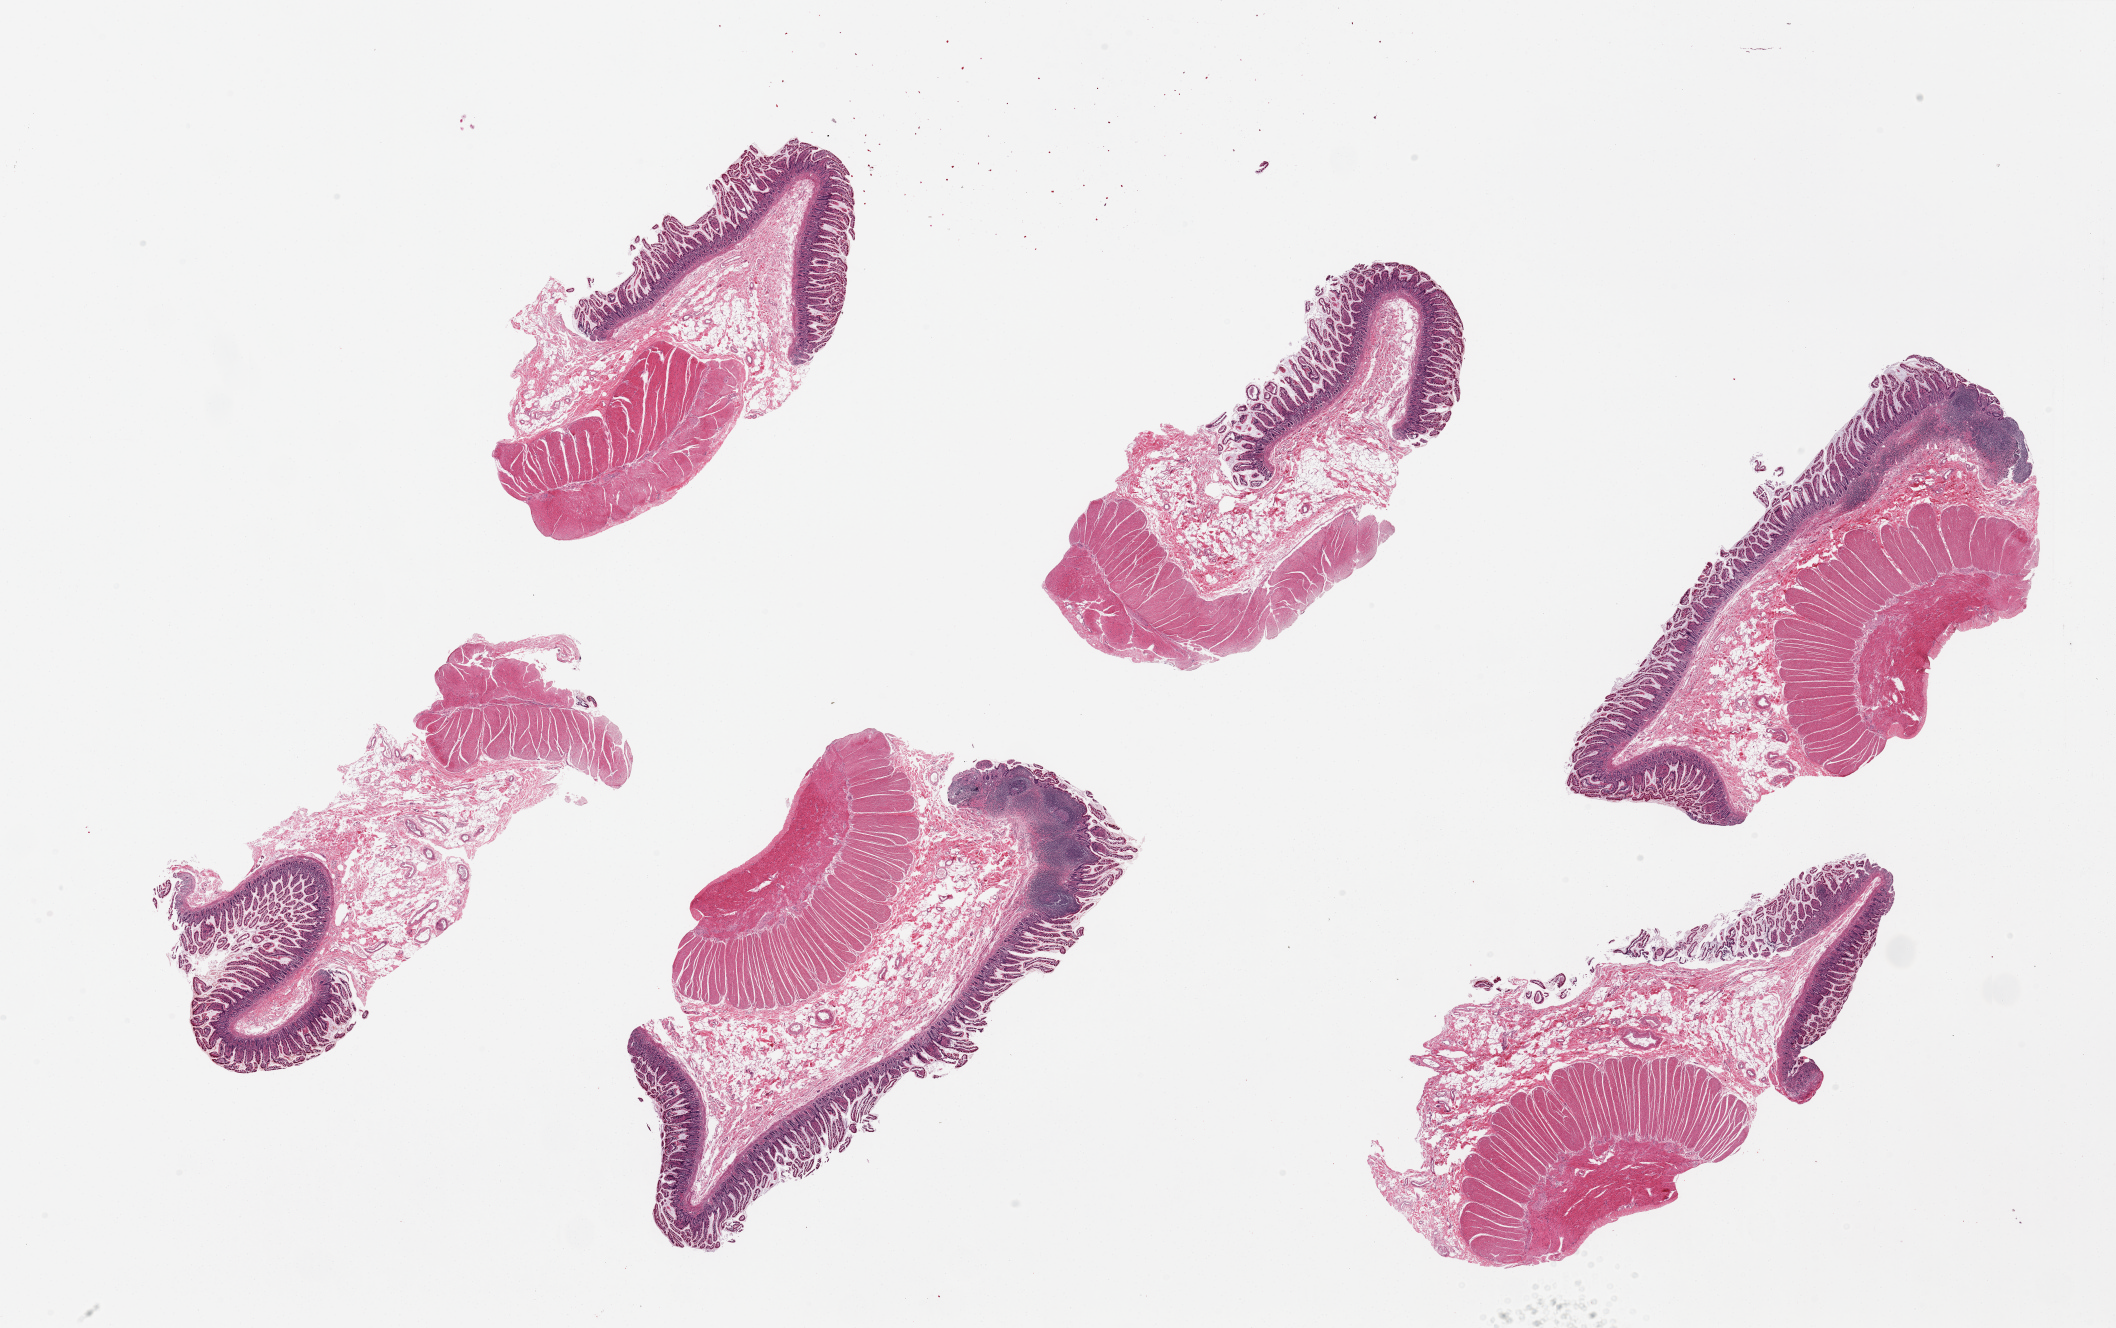
Digitized hematoxylin and eosin (H&E)-stained section — whole scanned area (about 33.5 x 21.0 mm) shown as a low-resolution overview. PAXgene-fixed, paraffin-embedded tissue. Sampled site (target tissue): ileum. Tissue donor sample. Donor: male.
* pathologist's review note for this sample: 6 pieces, all containing muscularis (not target), lymphoid nodules